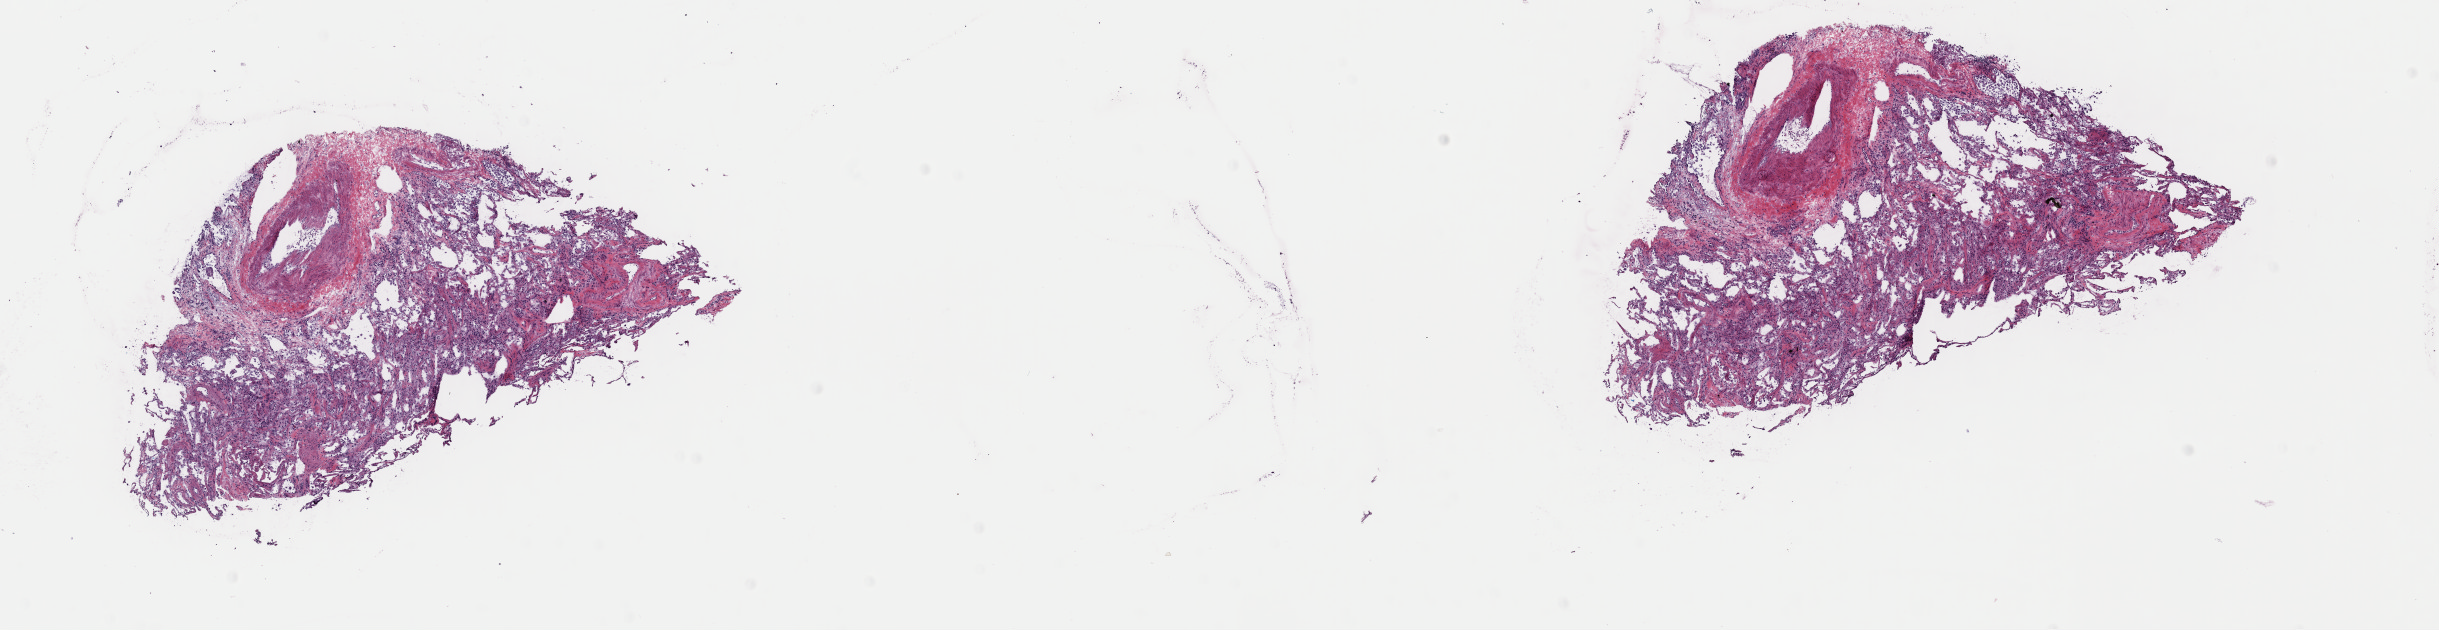
Whole-slide histology image, H&E-stained, shown as a low-resolution overview of the whole scanned area (about 19.3 x 5.0 mm, slide scanned at 40x), frozen section from the top of the tissue portion, lung, primary tumour sample. Male patient; age at initial diagnosis 80 years. Slide review estimates, as recorded: tumour cells 60%, tumour nuclei 80%, normal cells 5%, stromal cells 35%, necrosis 0%. Infiltration values recorded for this section: lymphocyte infiltration 2%, monocyte infiltration 8%, neutrophil infiltration 2%.
* AJCC pathologic stage: IB (7th edition)
* pathologic diagnosis: Acinar cell carcinoma (upper lobe, lung)